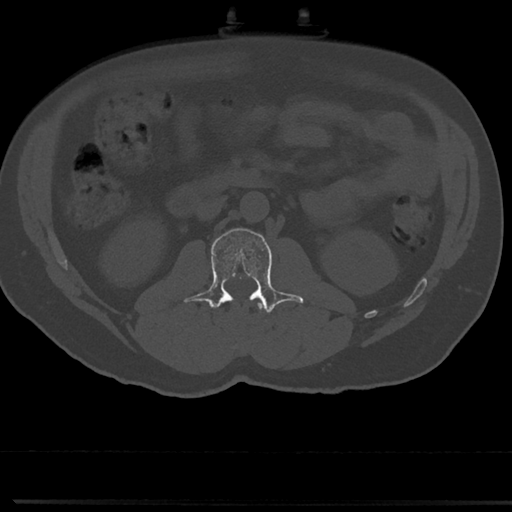
CT including the spine, one axial slice; position 21 of 817 along the scan axis; reconstruction kernel Br40s/3; bone window (W 1800 / L 400 HU); 0.5 mm slice thickness; 512 × 512 image matrix, field of view 355 × 355 mm. Male patient, age 61 years. Case-level facts recorded for this patient, not image findings: primary cancer: prostate.
Outlined on this slice (semi-automatically segmented with operator editing):
- L1 vertebra: bounding box (x1, y1, x2, y2) in pixels: (241, 302, 262, 342)
- L2 vertebra: (191, 228, 304, 313)